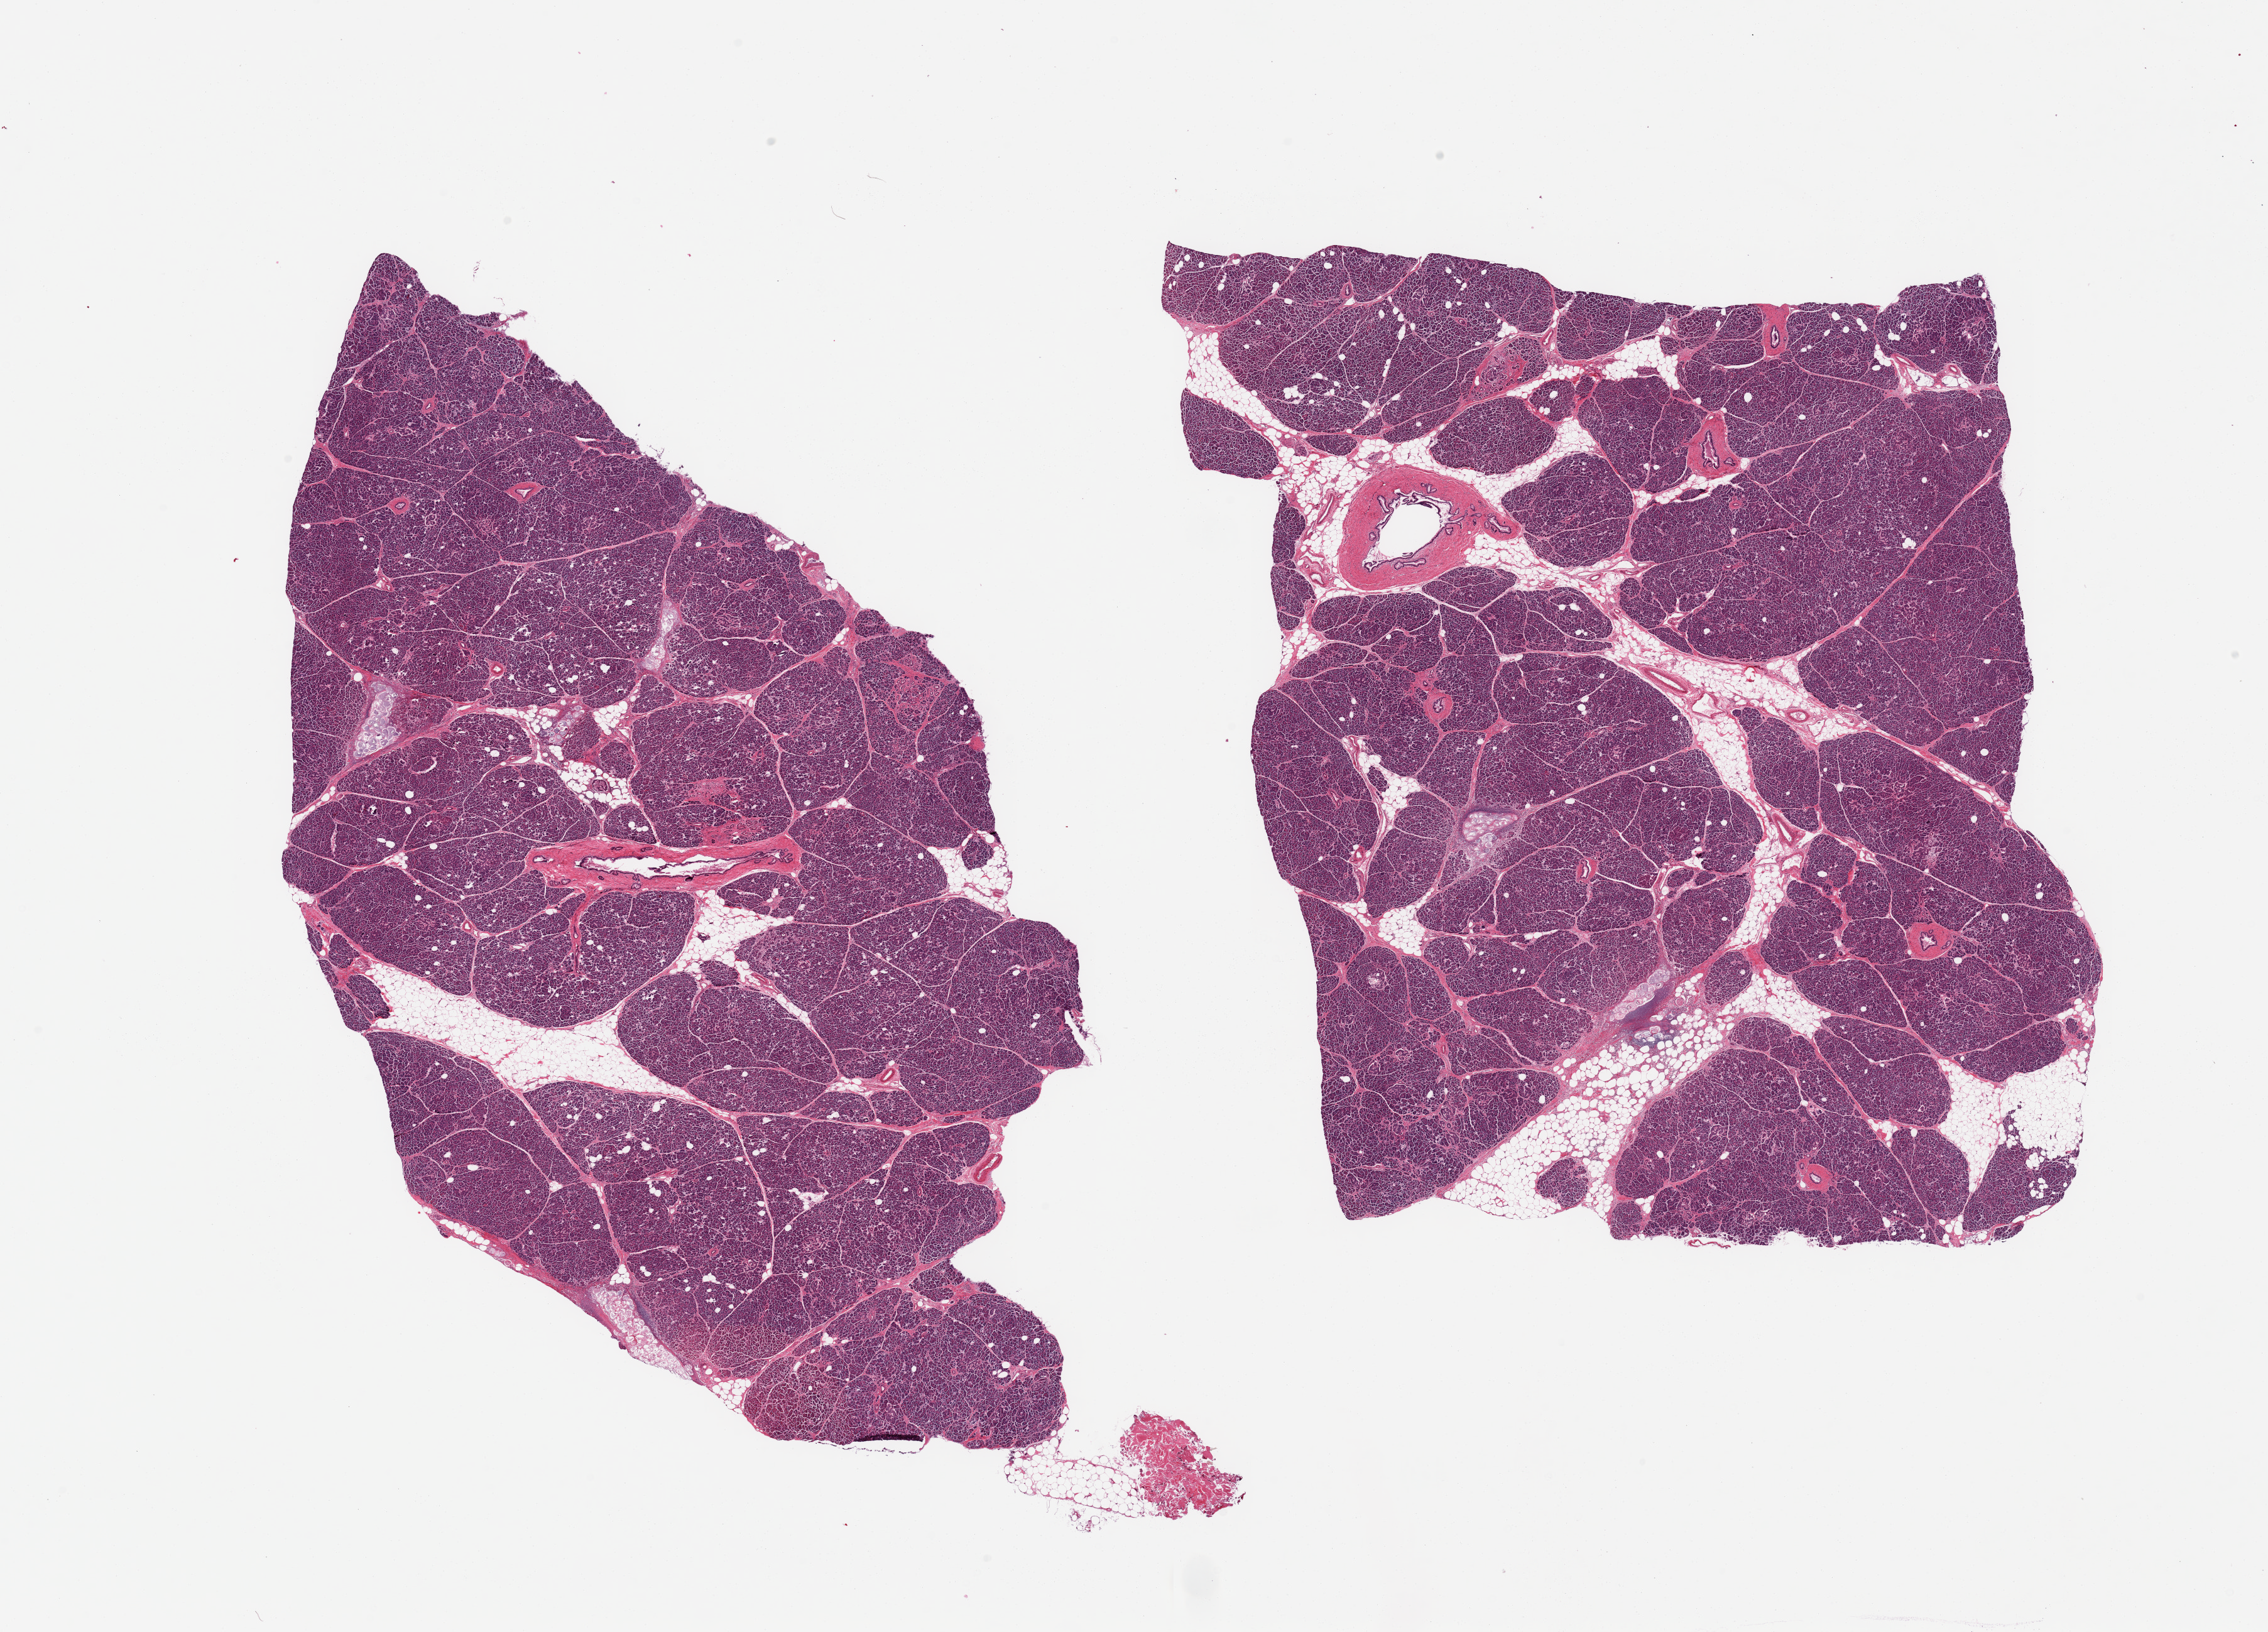
Digitized H&E-stained section, shown as a low-resolution overview of the whole scanned area (about 28.5 x 20.5 mm, from a 20x scan), PAXgene-fixed, paraffin-embedded tissue, section of pancreas (target tissue), tissue donor sample. Male donor.
Pathologist's review note for this sample: 2 pieces, islets rare, degenerating, cystic metaplasia.